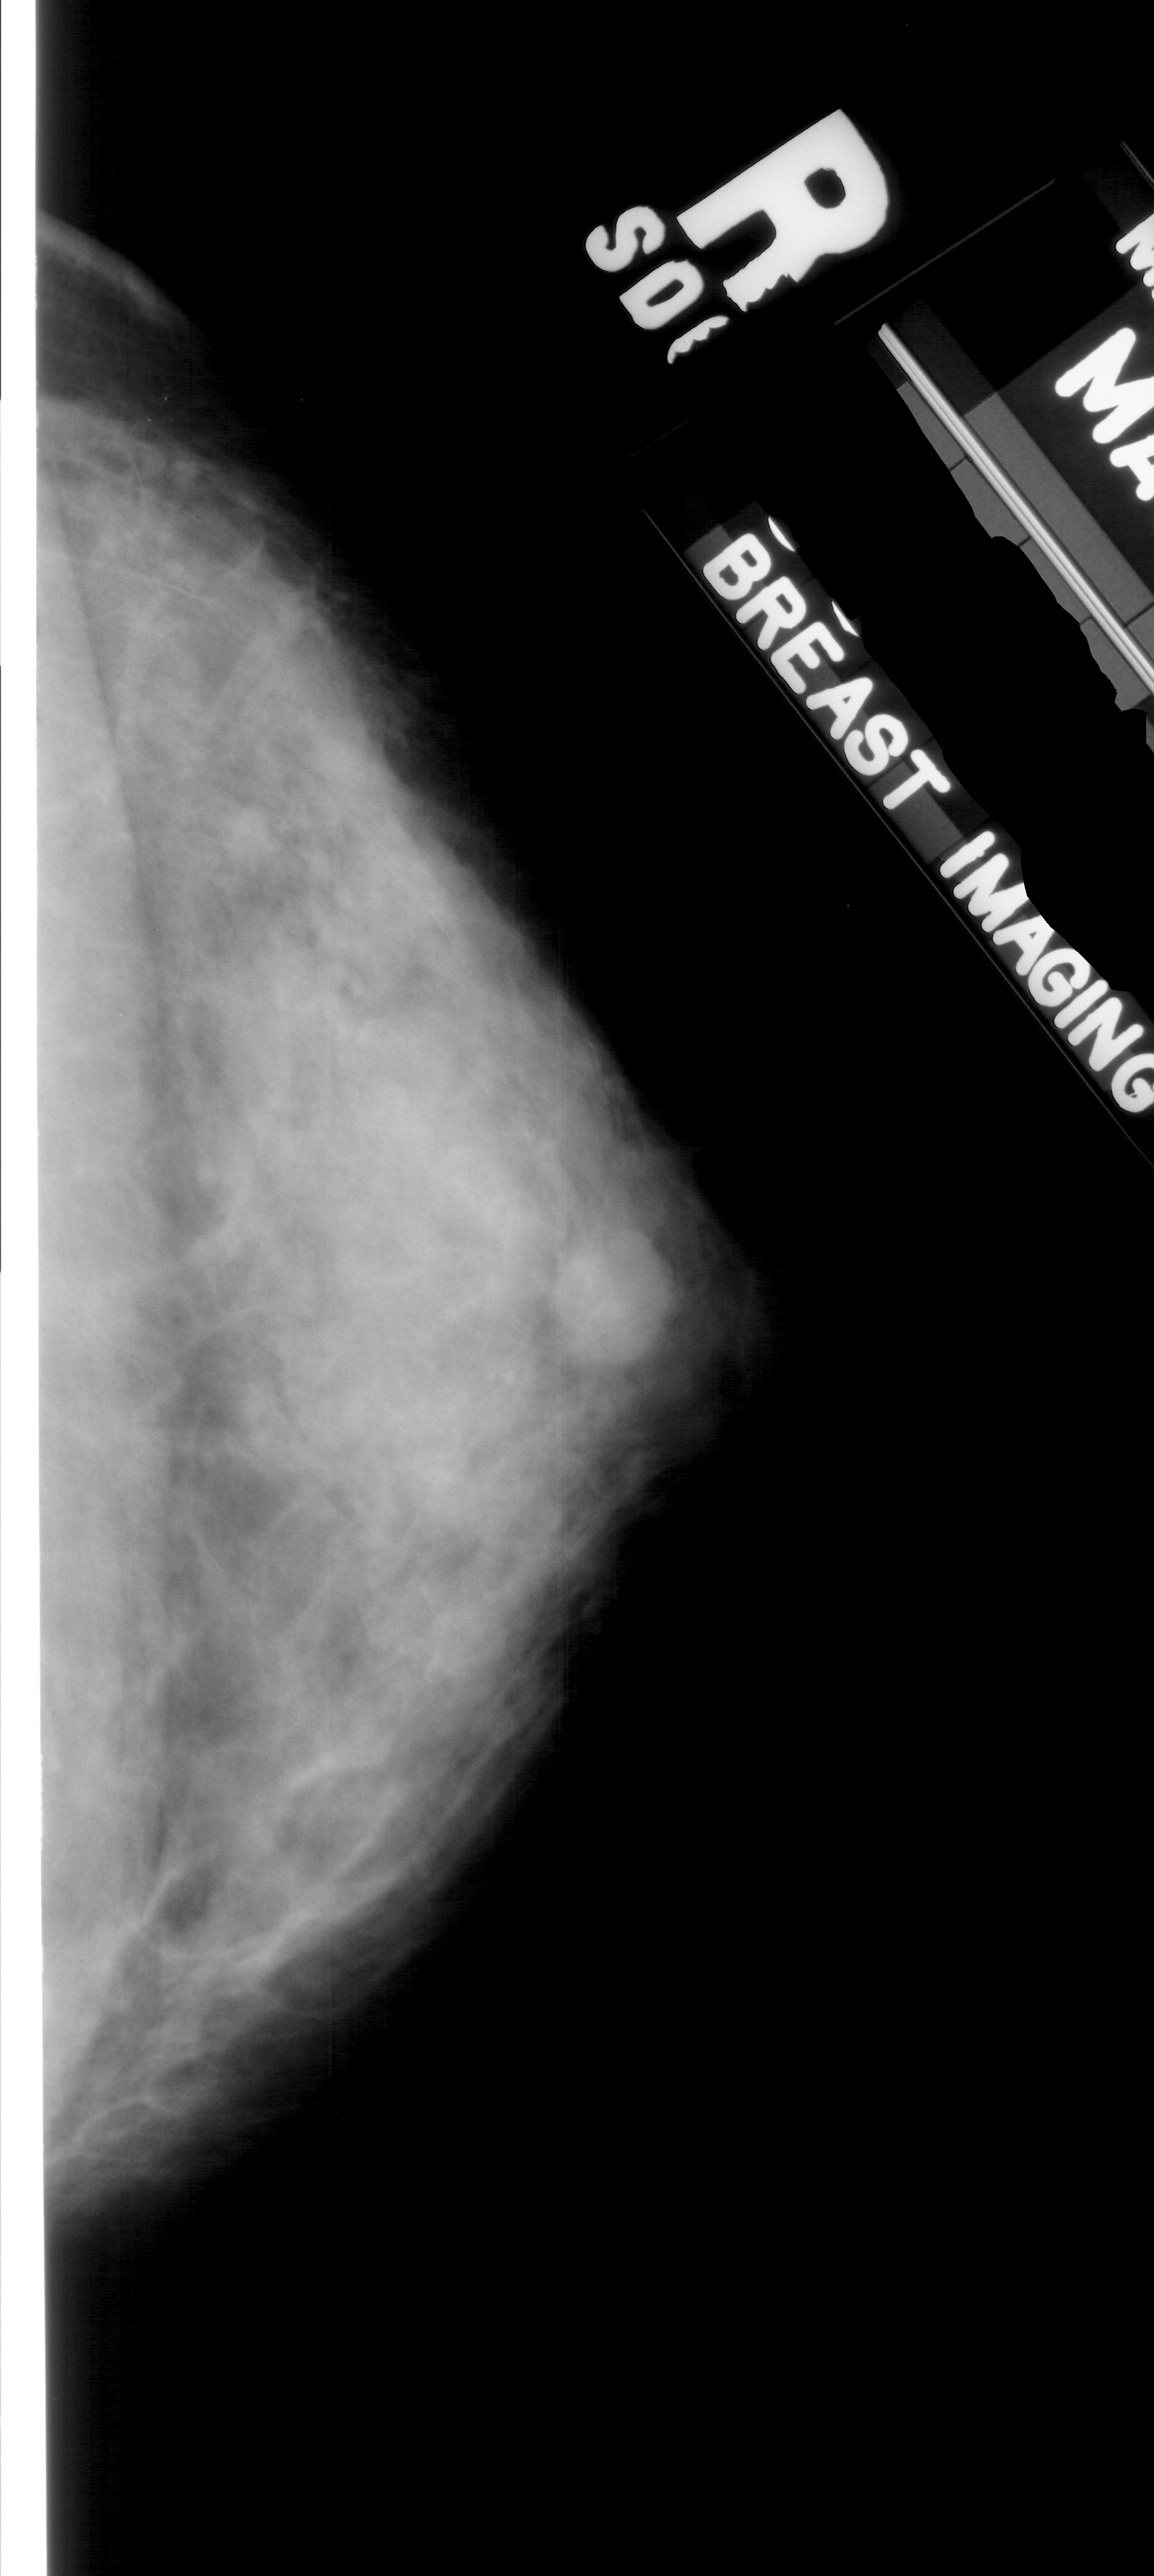
Scanned film-screen mammogram. Right breast. CC view. BI-RADS breast density category 4 (scale 1–4). 1154 × 2576 image matrix.
Expert-marked regions of interest on this image (one box per marked abnormality):
- mass, shape lobulated, margins microlobulated; BI-RADS assessment category 4; subtlety rating 4 on a 1 (subtle) to 5 (obvious) scale; pathology (as recorded): benign: bounding box [x1, y1, x2, y2] px = [529, 1229, 714, 1381]